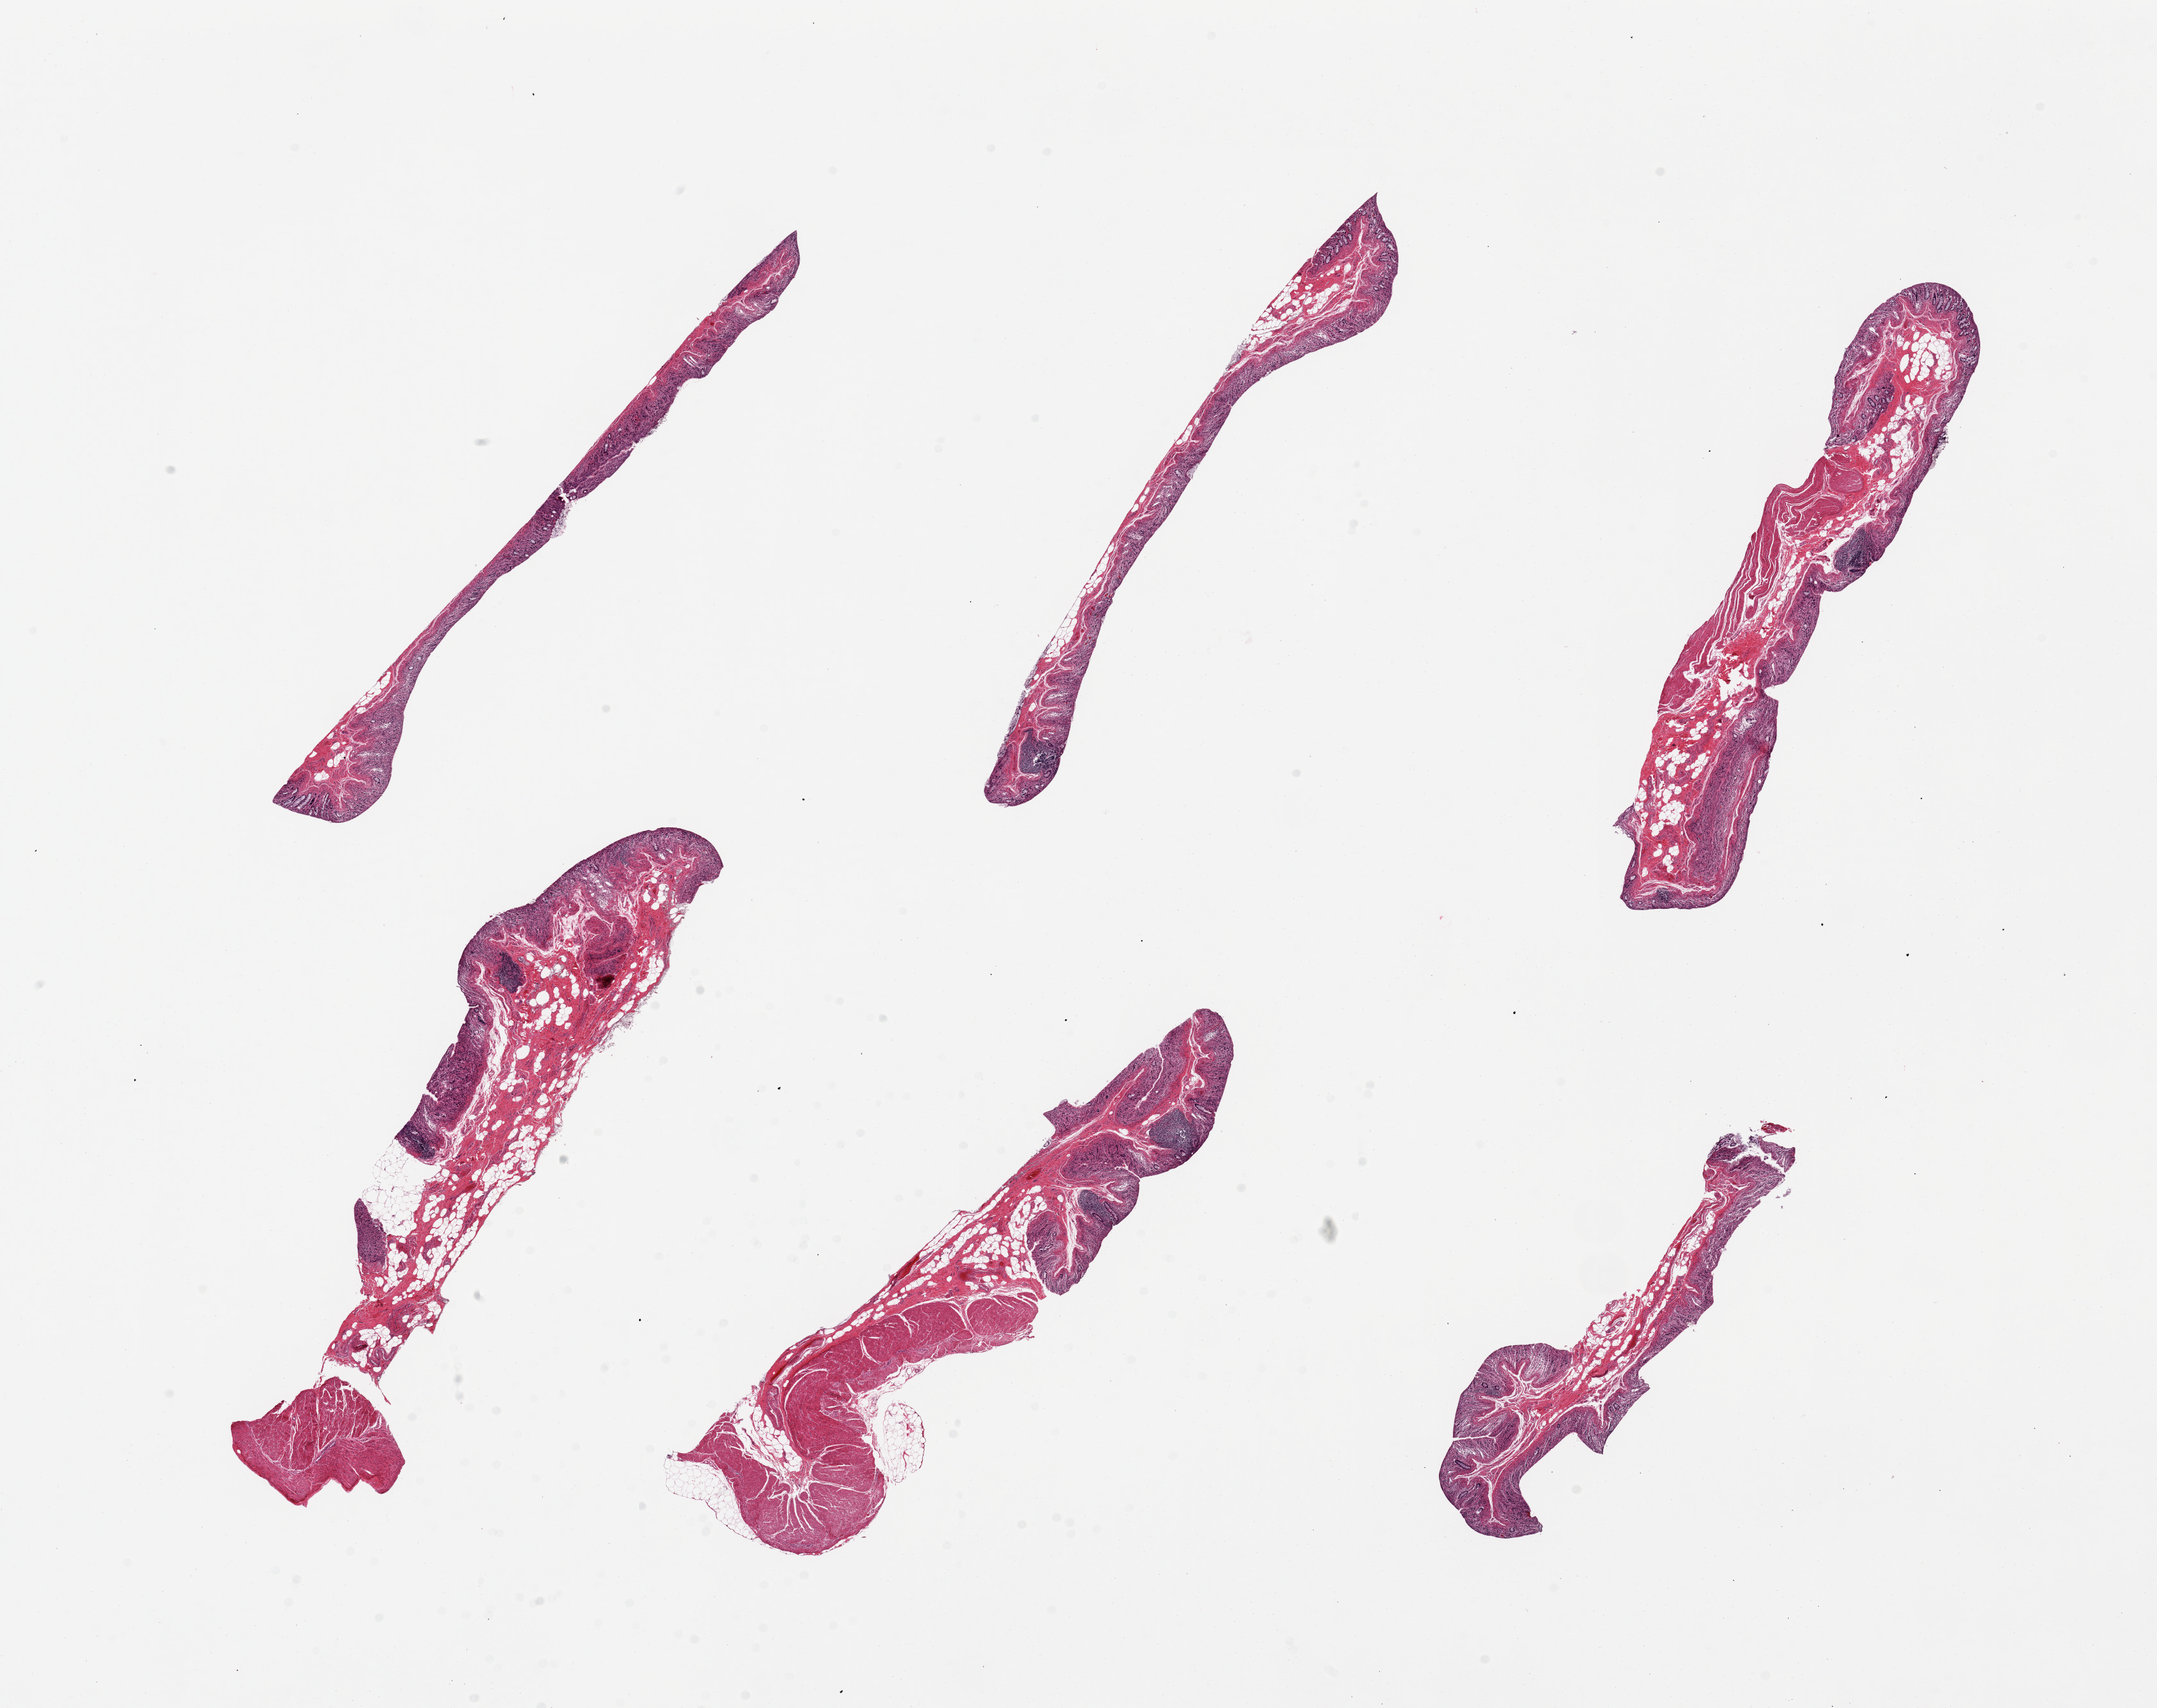
H&E whole-slide image — shown as a low-resolution overview of the whole scanned area (about 26.6 x 21.0 mm, slide scanned at 20x); PAXgene-fixed paraffin-embedded (PFPE) section; sampled site (target tissue): transverse colon; donor tissue sample.
* review note (as recorded): 6 pieces, up to 10x3mm; ~50% badly autolyzed mucosa, rest is muscle & fat